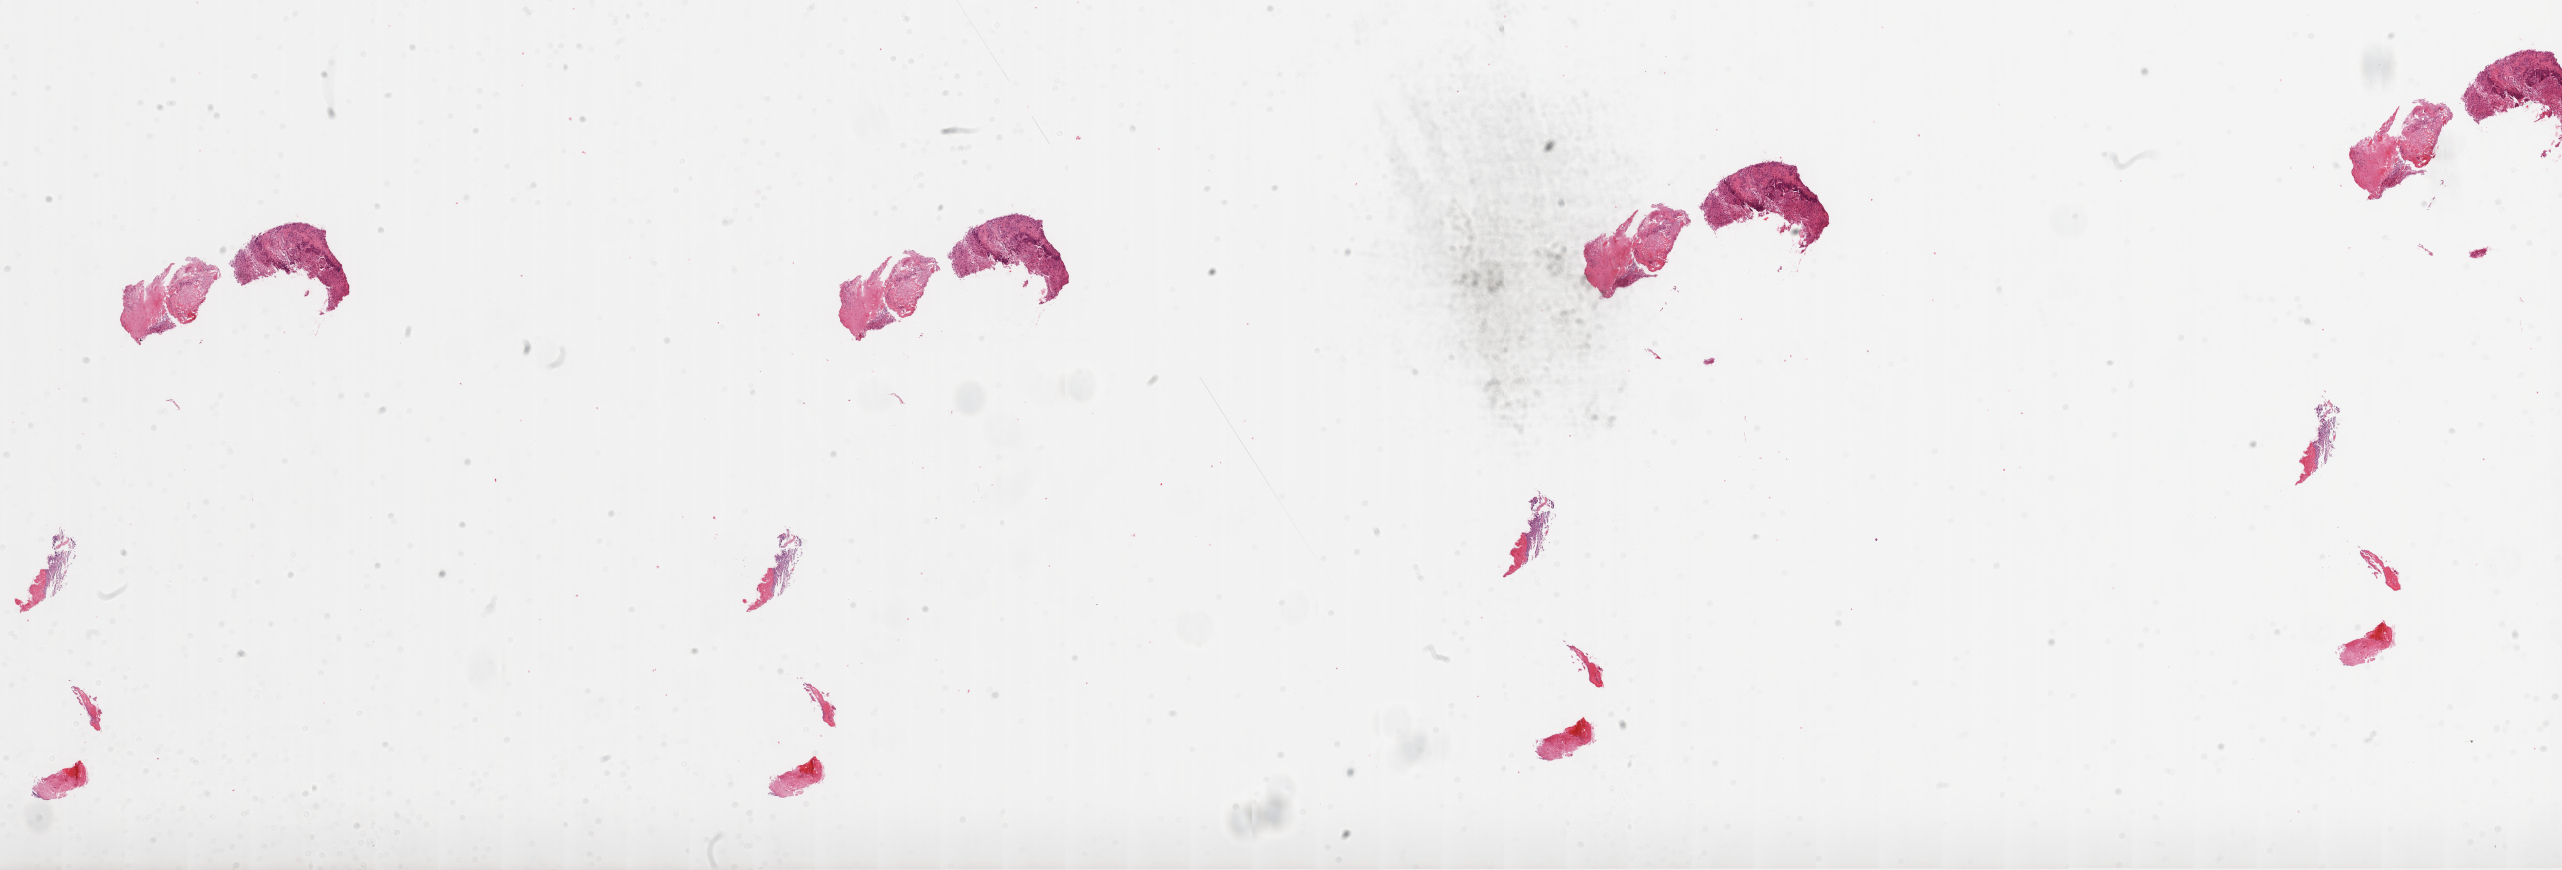
Whole-slide histology image, Hematoxylin and eosin (H&E) stained — whole scanned area (about 41.1 x 14.0 mm, slide scanned at 20x) shown as a low-resolution overview; formalin-fixed paraffin-embedded (FFPE) diagnostic section; brain, primary tumour sample. Patient: male, age at initial diagnosis 79 years.
Diagnosis: Glioblastoma.